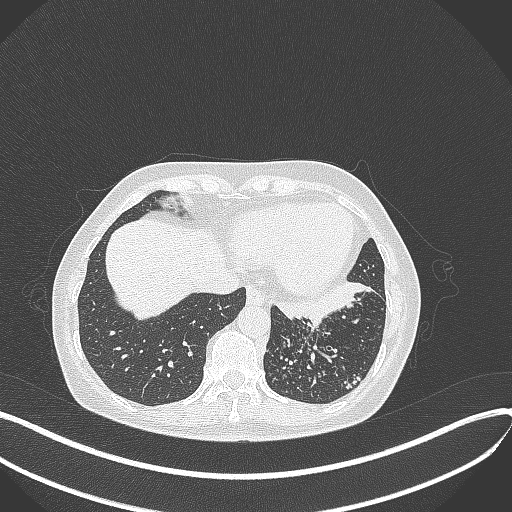
Chest CT, one axial slice. 100 kVp. Lung window (W 1500 / L -600 HU). 1 mm slice thickness. 512 × 512 image matrix, field of view 400 × 400 mm. Patient: female, 63 years. Case-level facts recorded for this patient, not image findings: clinical TNM (as recorded): T1b N0 M0; histopathological grade: G2-3.
Structures marked on this image (bounding box drawn by a radiologist):
- lung tumour (recorded histology: adenocarcinoma): box from (x=276, y=278) to (x=377, y=328) px